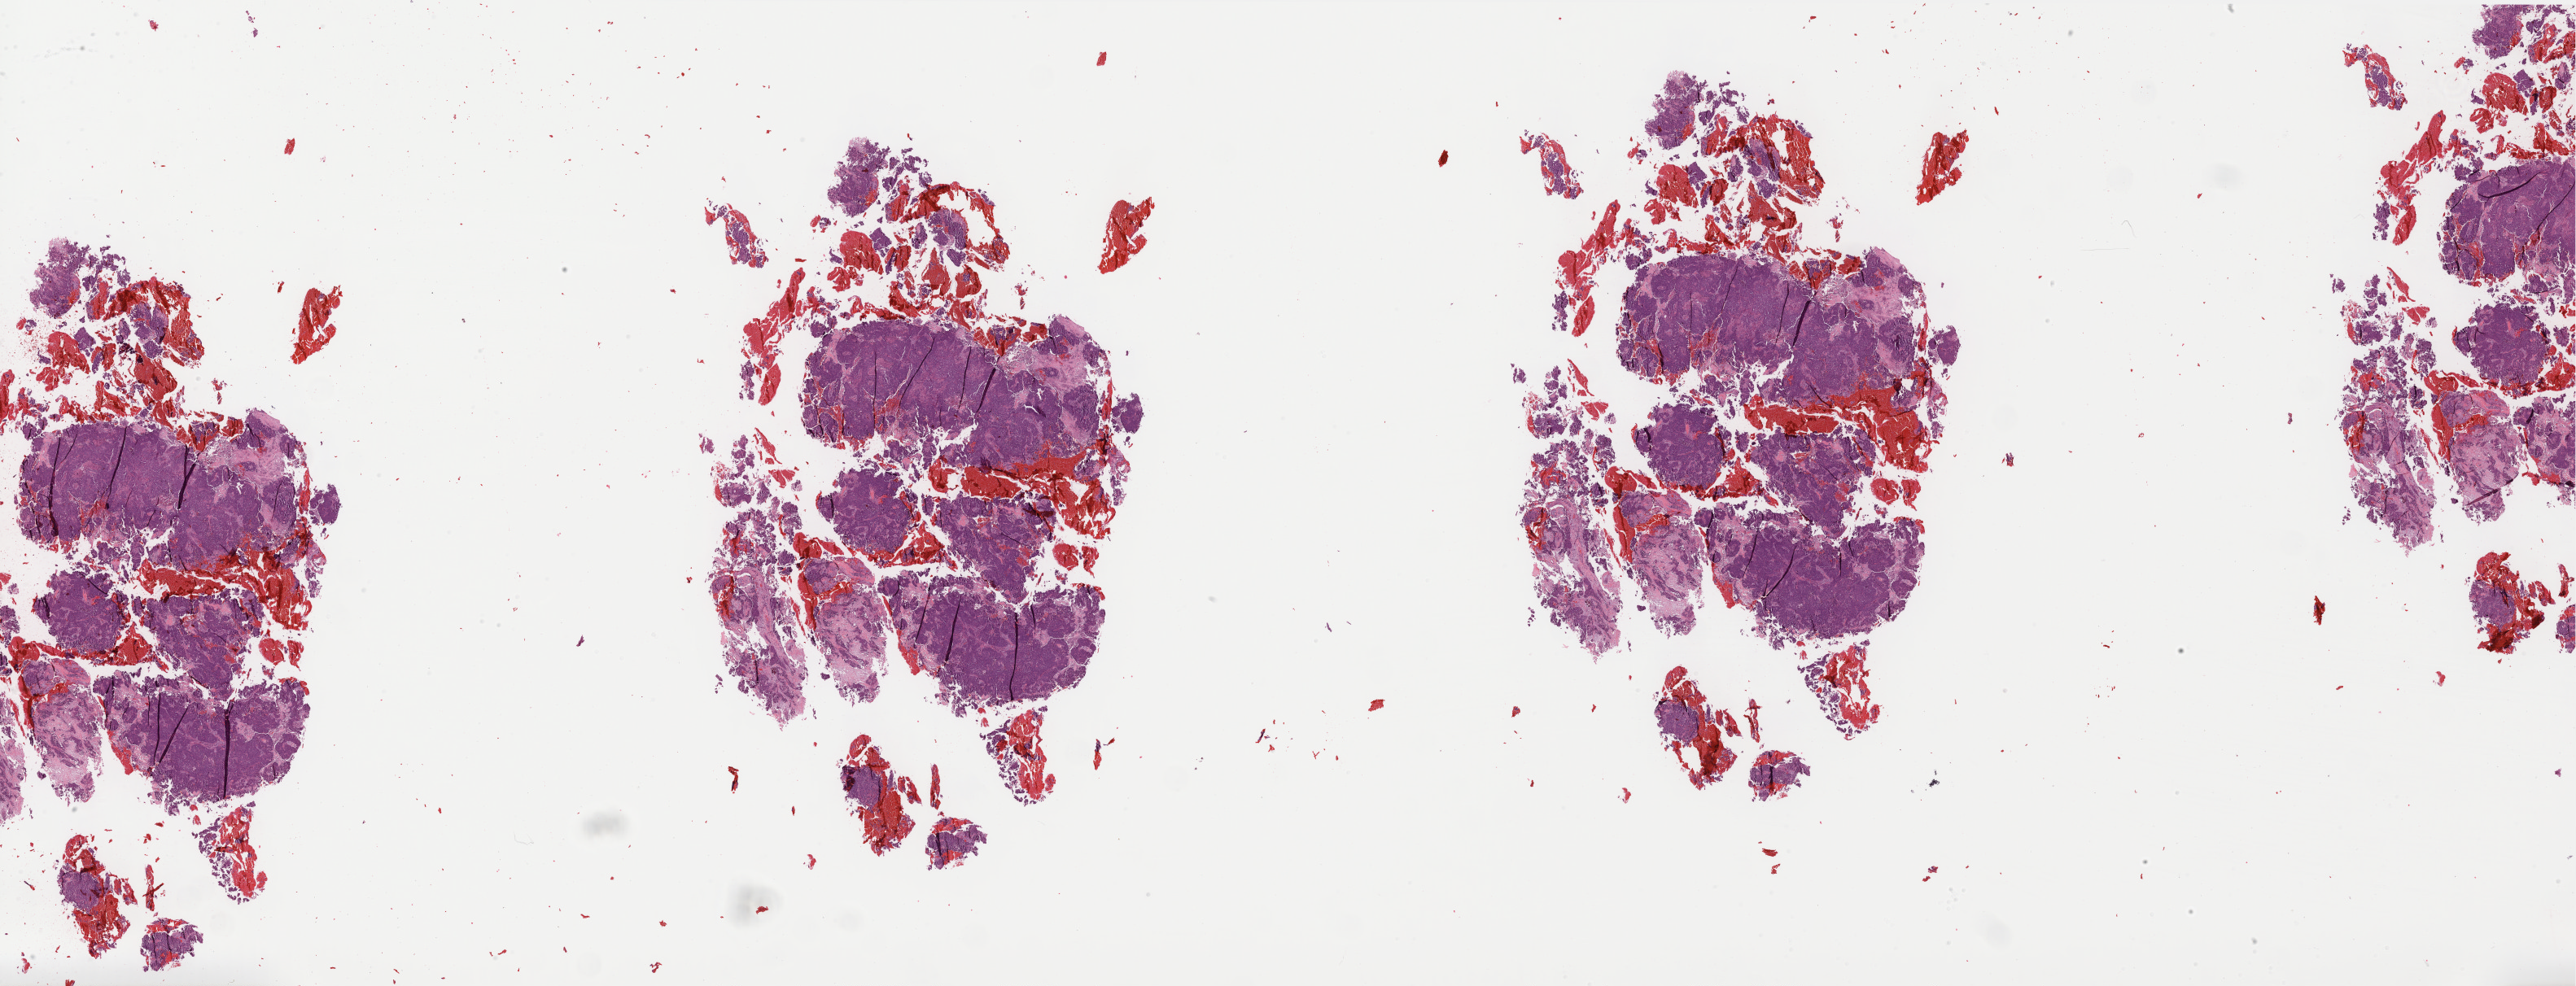
Digitized Hematoxylin and eosin (H&E) stained tissue section (whole slide) — low-resolution overview of the scanned area, about 50.7 x 19.4 mm, FFPE section, sample: primary tumour, cervix. Female patient; age at initial diagnosis 55 years. Histologic grade: G3 (poorly differentiated).
Histologic diagnosis: Squamous cell carcinoma, NOS (cervix uteri). FIGO stage: IIB.